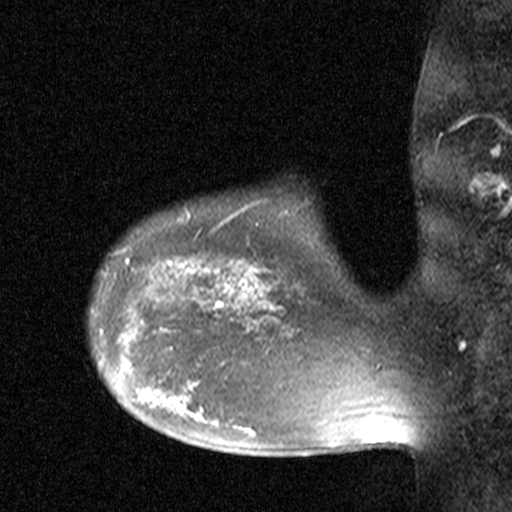
Breast MRI (dynamic contrast-enhanced), one sagittal slice. Position 35 of 44 along the scan axis. Dynamic contrast-enhanced study with each time point stored as its own series, time point 2 of 3 at this slice position (early post-contrast, ordered by acquisition time). 1.5 T. TE 4.5 ms, TR 11 ms. 3 mm slice thickness. 512 × 512 image matrix, field of view 200 × 200 mm. Patient: female, 38 years. Case-level facts recorded for this patient, not image findings: setting: breast cancer imaged before/during neoadjuvant chemotherapy; receptor status: HR-positive, HER2-negative.
Outlined on this slice (semi-automatically segmented with operator editing):
- analysis volume of interest (the breast-tissue region the enhancement analysis was run in; not a lesion): bounding box <176,272,251,349> (left, top, right, bottom; pixels)
- tumour enhancement mask (voxels above the 90 % enhancement threshold inside the analysis volume of interest): <214,283,248,330>